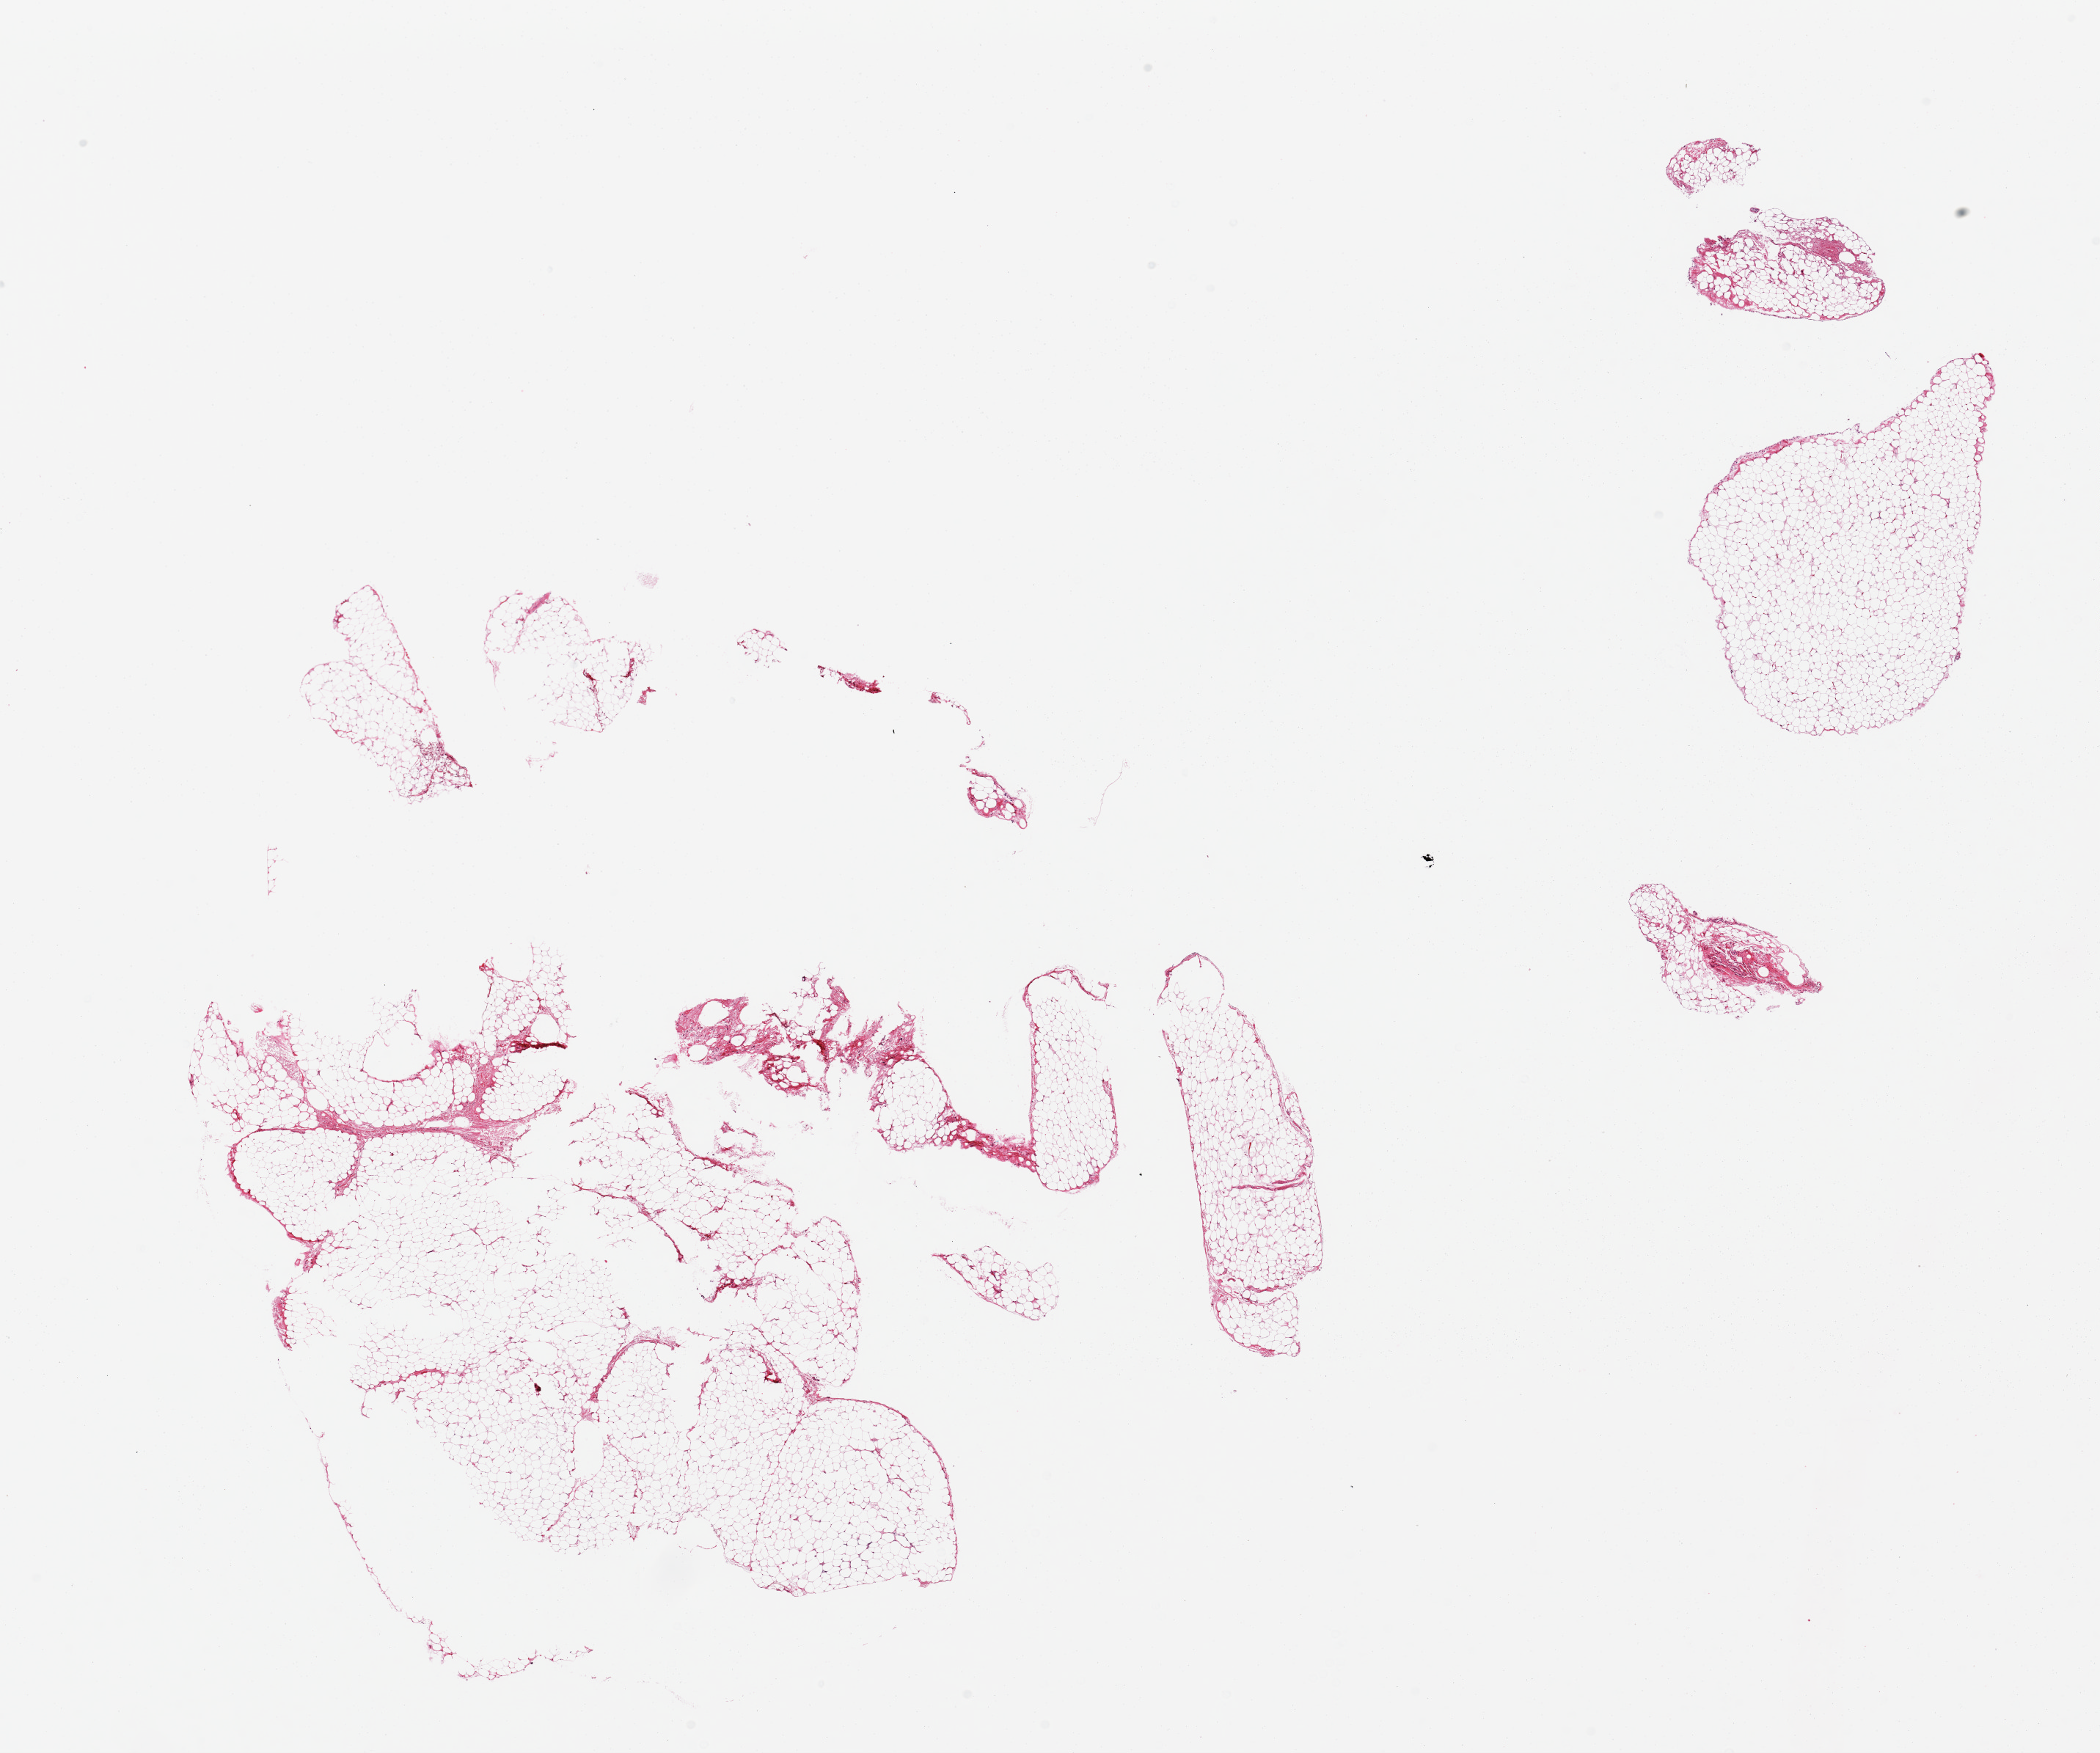
Hematoxylin and eosin (H&E) whole-slide image, a low-resolution overview of the entire scanned area, about 22.6 x 18.9 mm; PAXgene-fixed paraffin-embedded (PFPE) section; target tissue: omentum; donor tissue sample. Male donor.
Reviewer comment on this tissue sample: 2 pieces, fragmented, ~10% fascia/mesothelial hyperplasia.